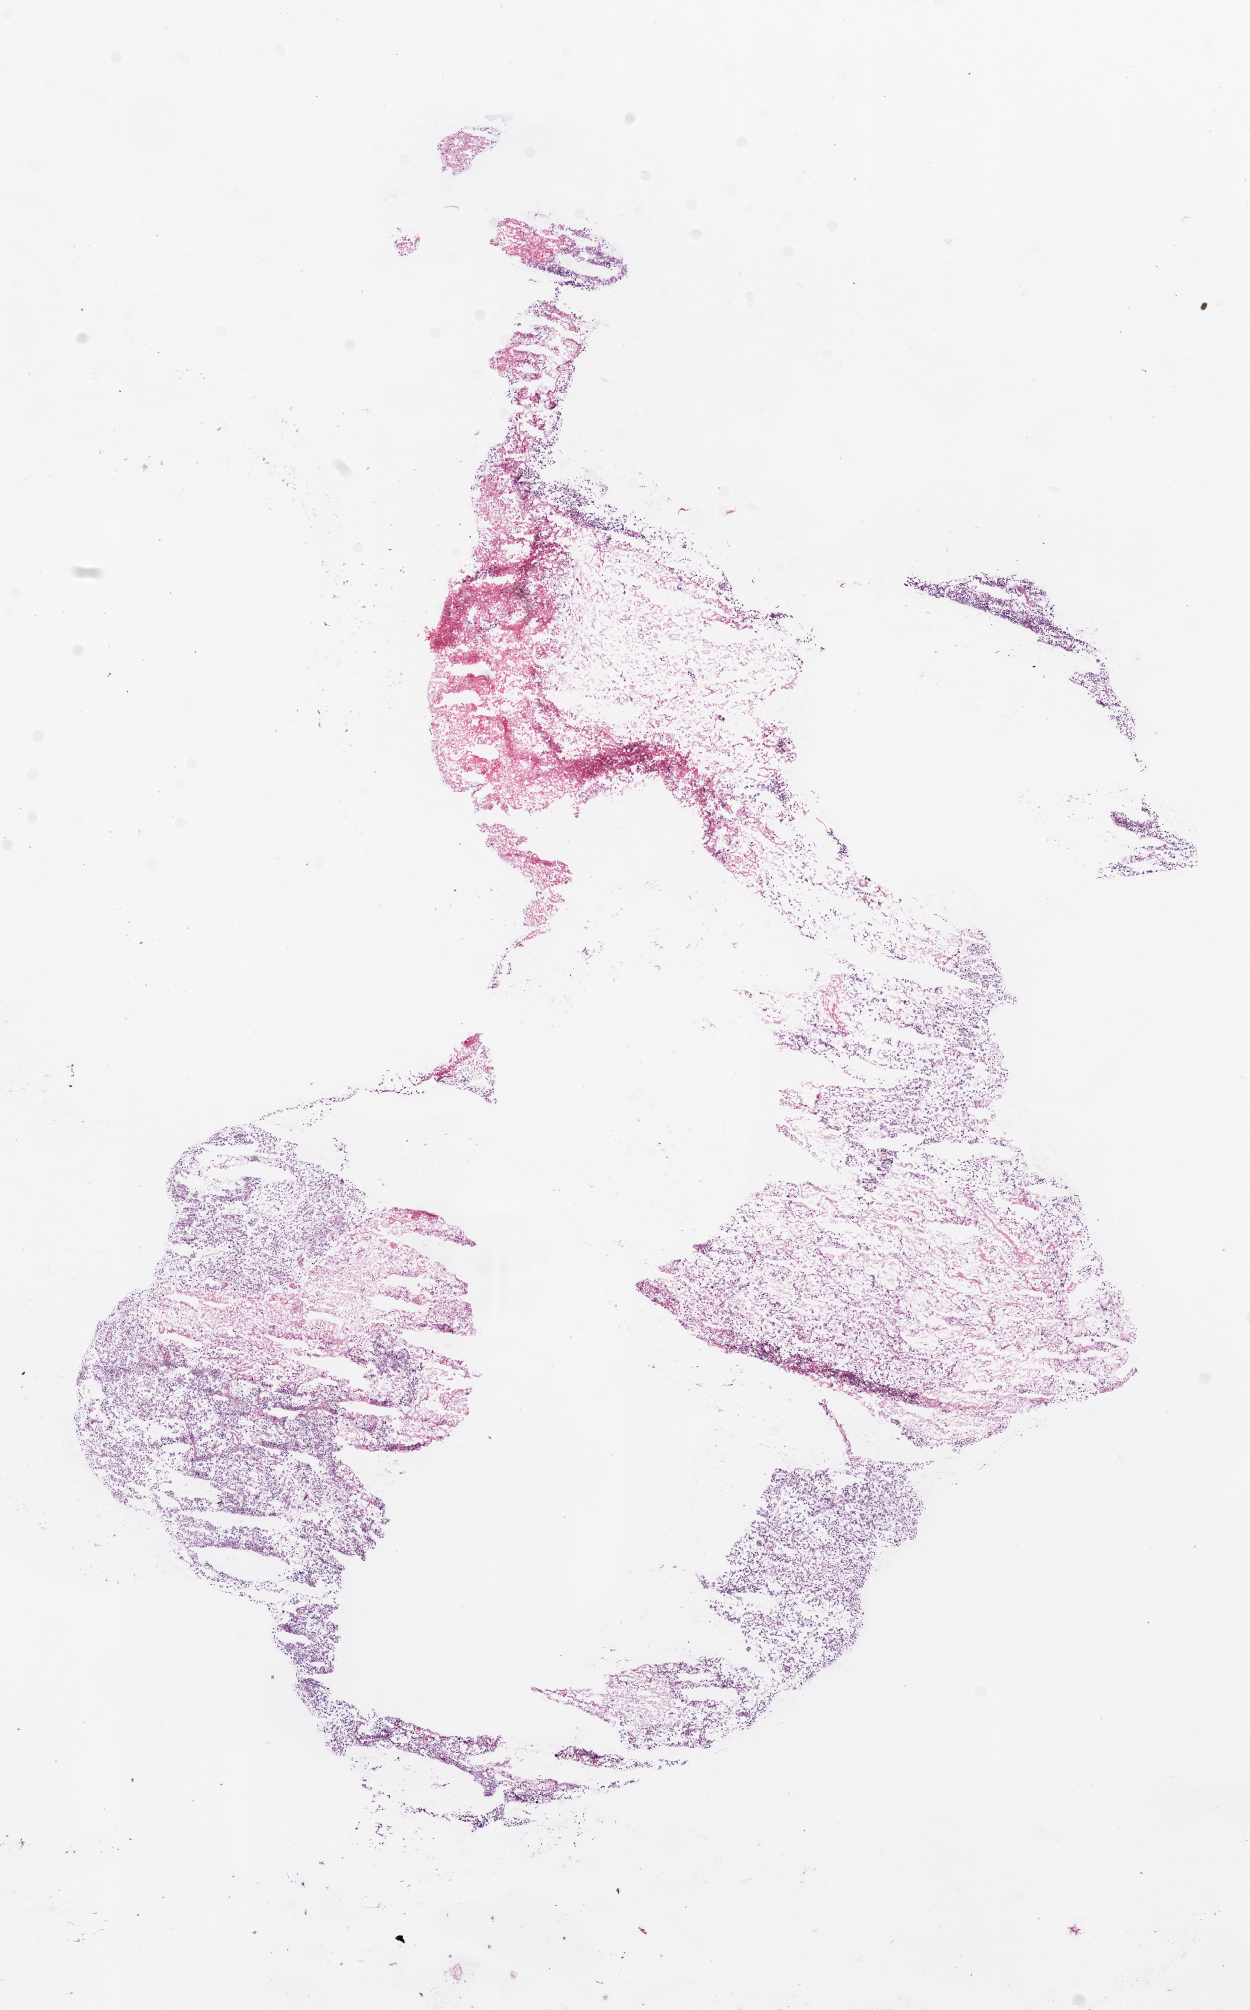
Digitized H&E tissue section (whole slide) — a low-resolution overview of the entire scanned area, about 10.0 x 16.1 mm (from a 20x scan). Frozen section. Primary tumour sample from the brain. Male patient; age at initial diagnosis 43 years. Pathologist review of this section (percent, as recorded): tumour cells 90%, tumour nuclei 80%, normal cells 0%, stromal cells 0%, necrosis 10%.
* diagnosis: Glioblastoma